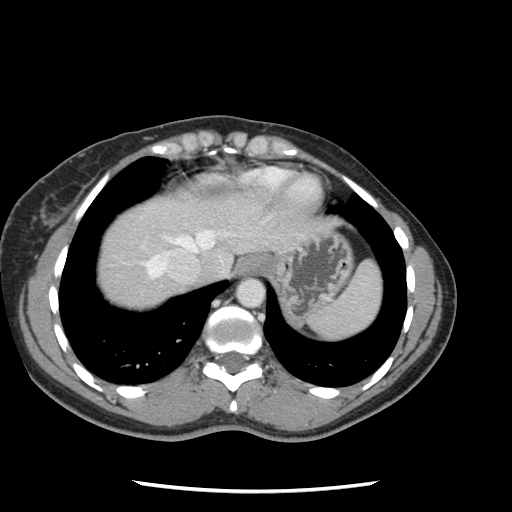
Contrast-enhanced abdominal CT, one axial slice. Position 108 of 134 along the scan axis. 120 kVp. Soft-tissue window (W 400 / L 40 HU). 2.5 mm slice thickness. 512 × 512 image matrix. Female patient, age 43 years. Case-level facts recorded for this patient, not image findings: diagnosis: colorectal cancer liver metastases, imaged before liver resection; multiple liver metastases: yes; largest metastasis: 3.4 cm; chemotherapy before resection: no.
Structures marked on this image (outlined manually by an expert reader):
- hepatic veins: bounding box <143,230,216,278> (left, top, right, bottom; pixels)
- liver: <96,197,280,310>
- planned liver remnant (the part of the liver to remain after resection): <97,198,203,295>
- portal vein (with intrahepatic branches): <141,246,143,249>